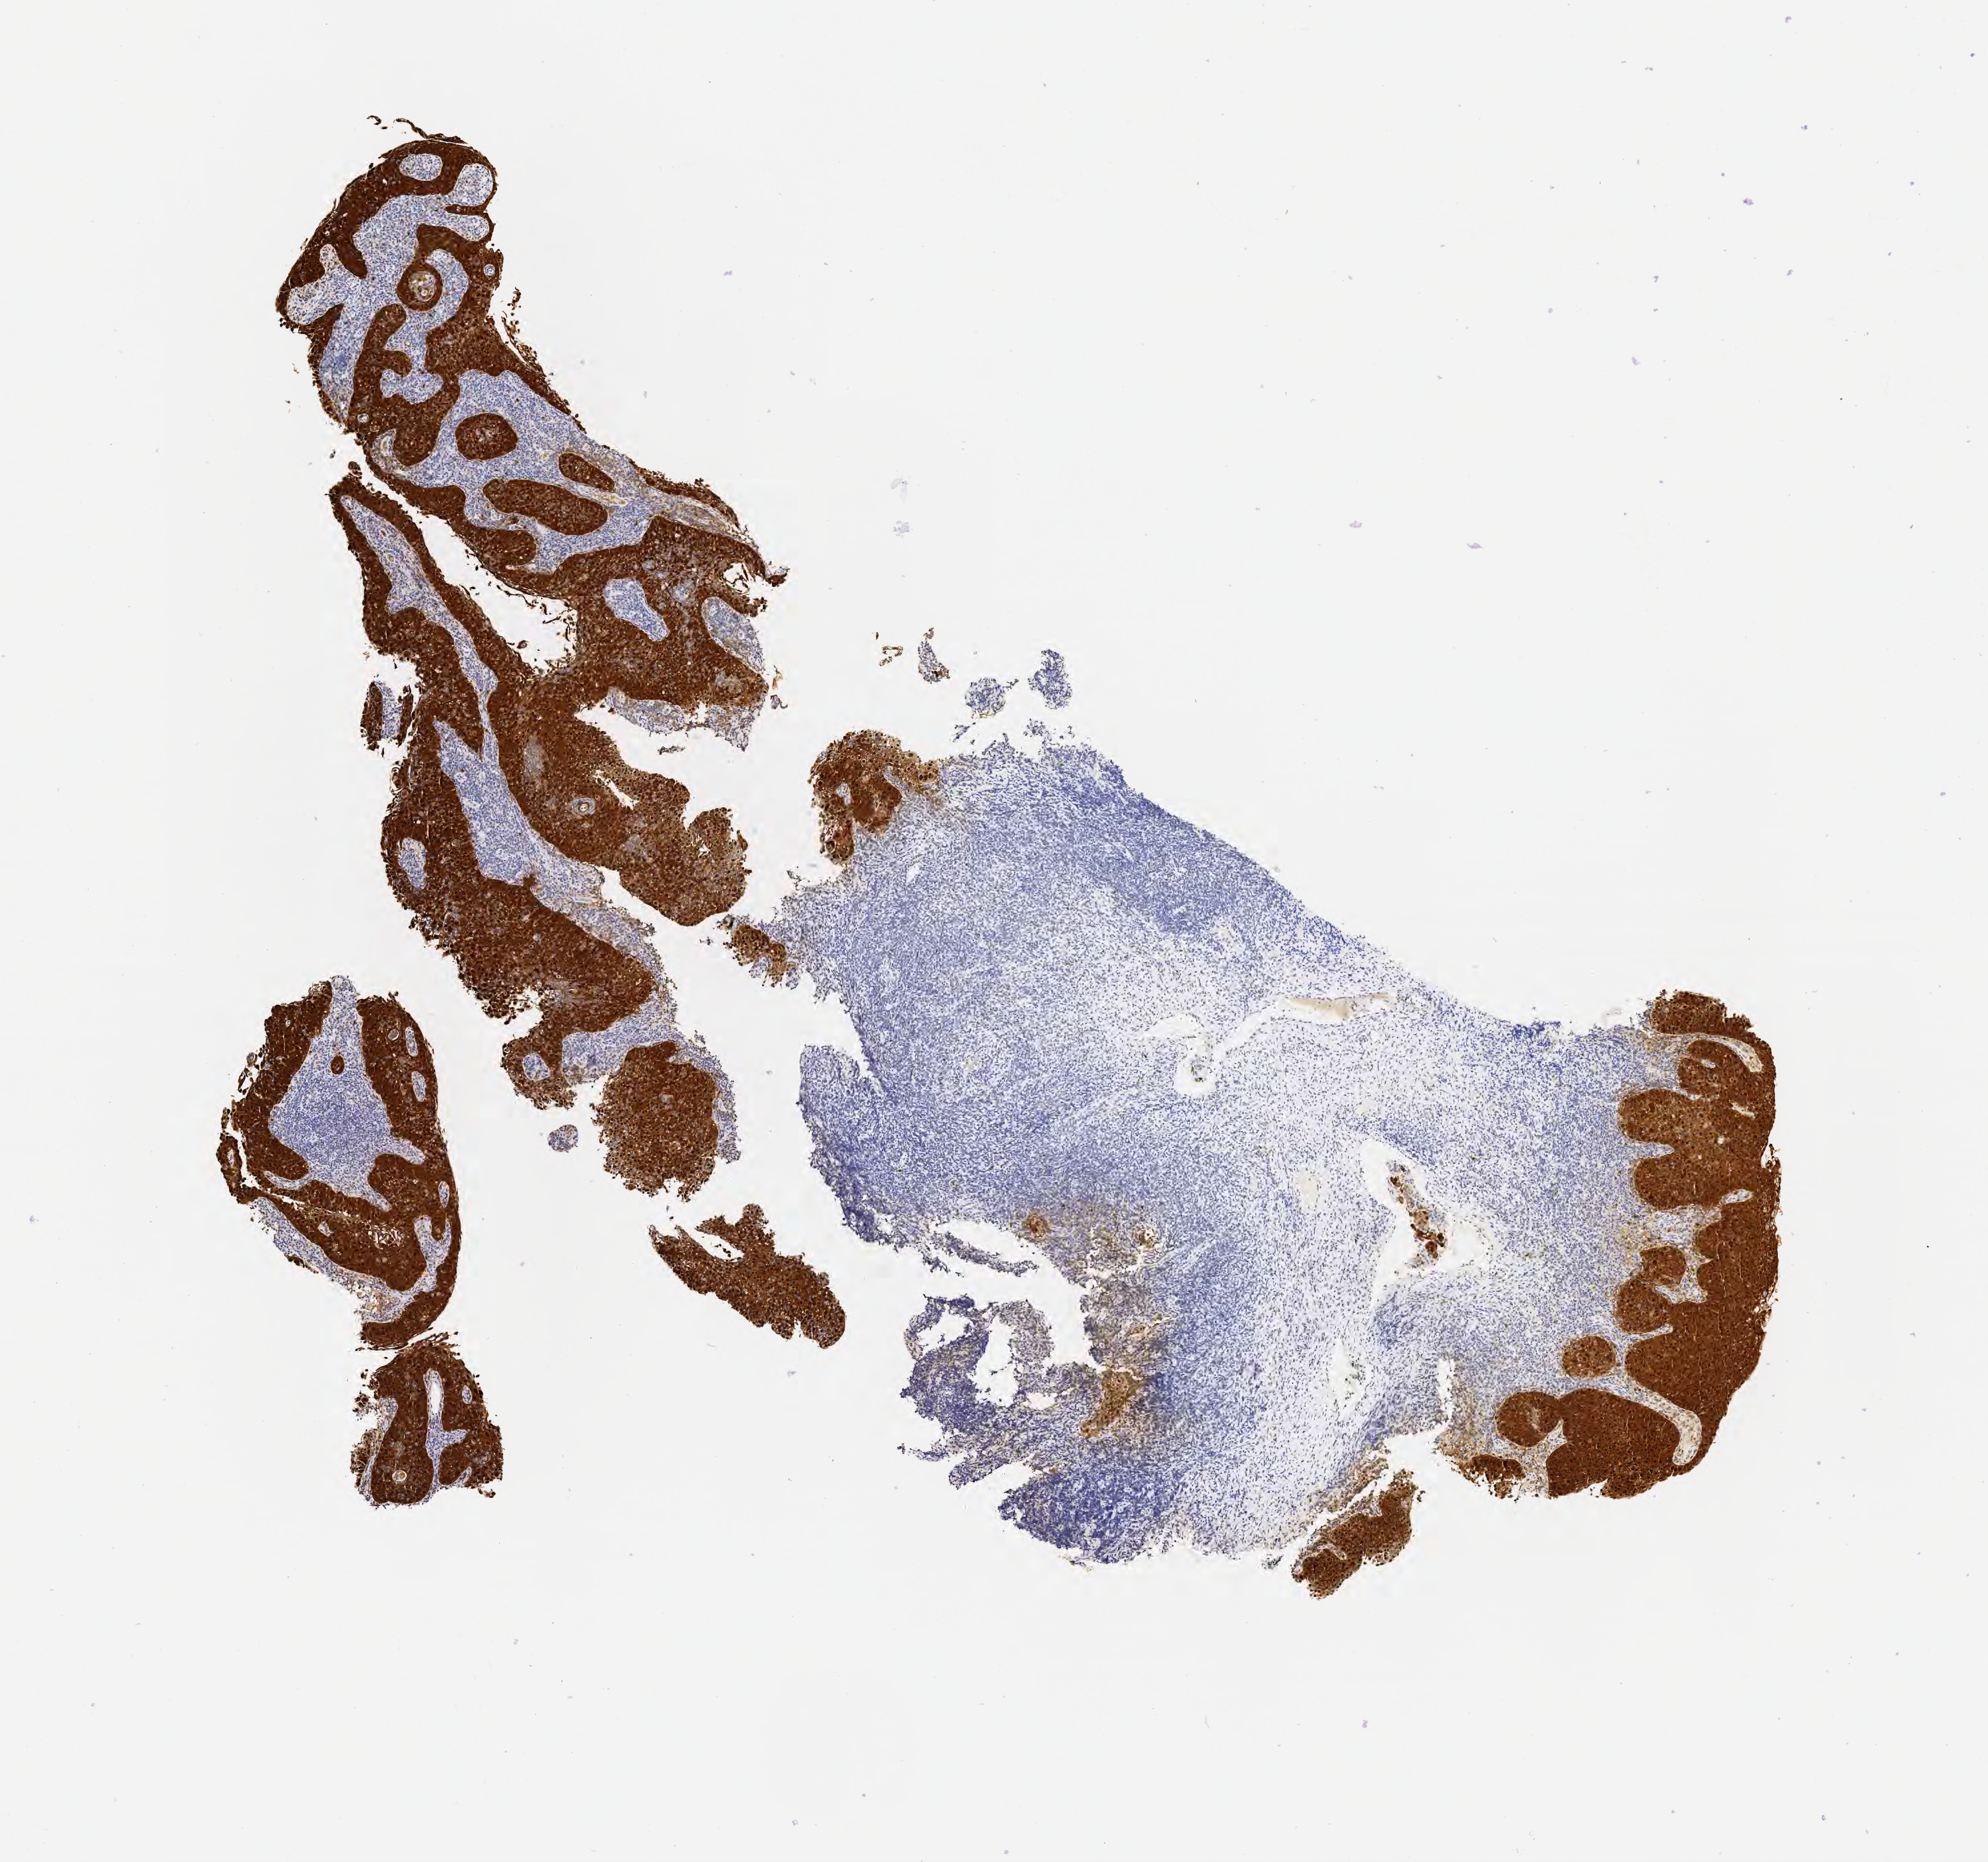
IHC for p16 (p16INK4a), whole-slide image — low-resolution overview of the scanned area, about 6.0 x 5.7 mm; tumor tissue; site: cervix. Patient female; 52 years old.
Histologic diagnosis: Squamous cell carcinoma, large cell, nonkeratinizing, NOS.